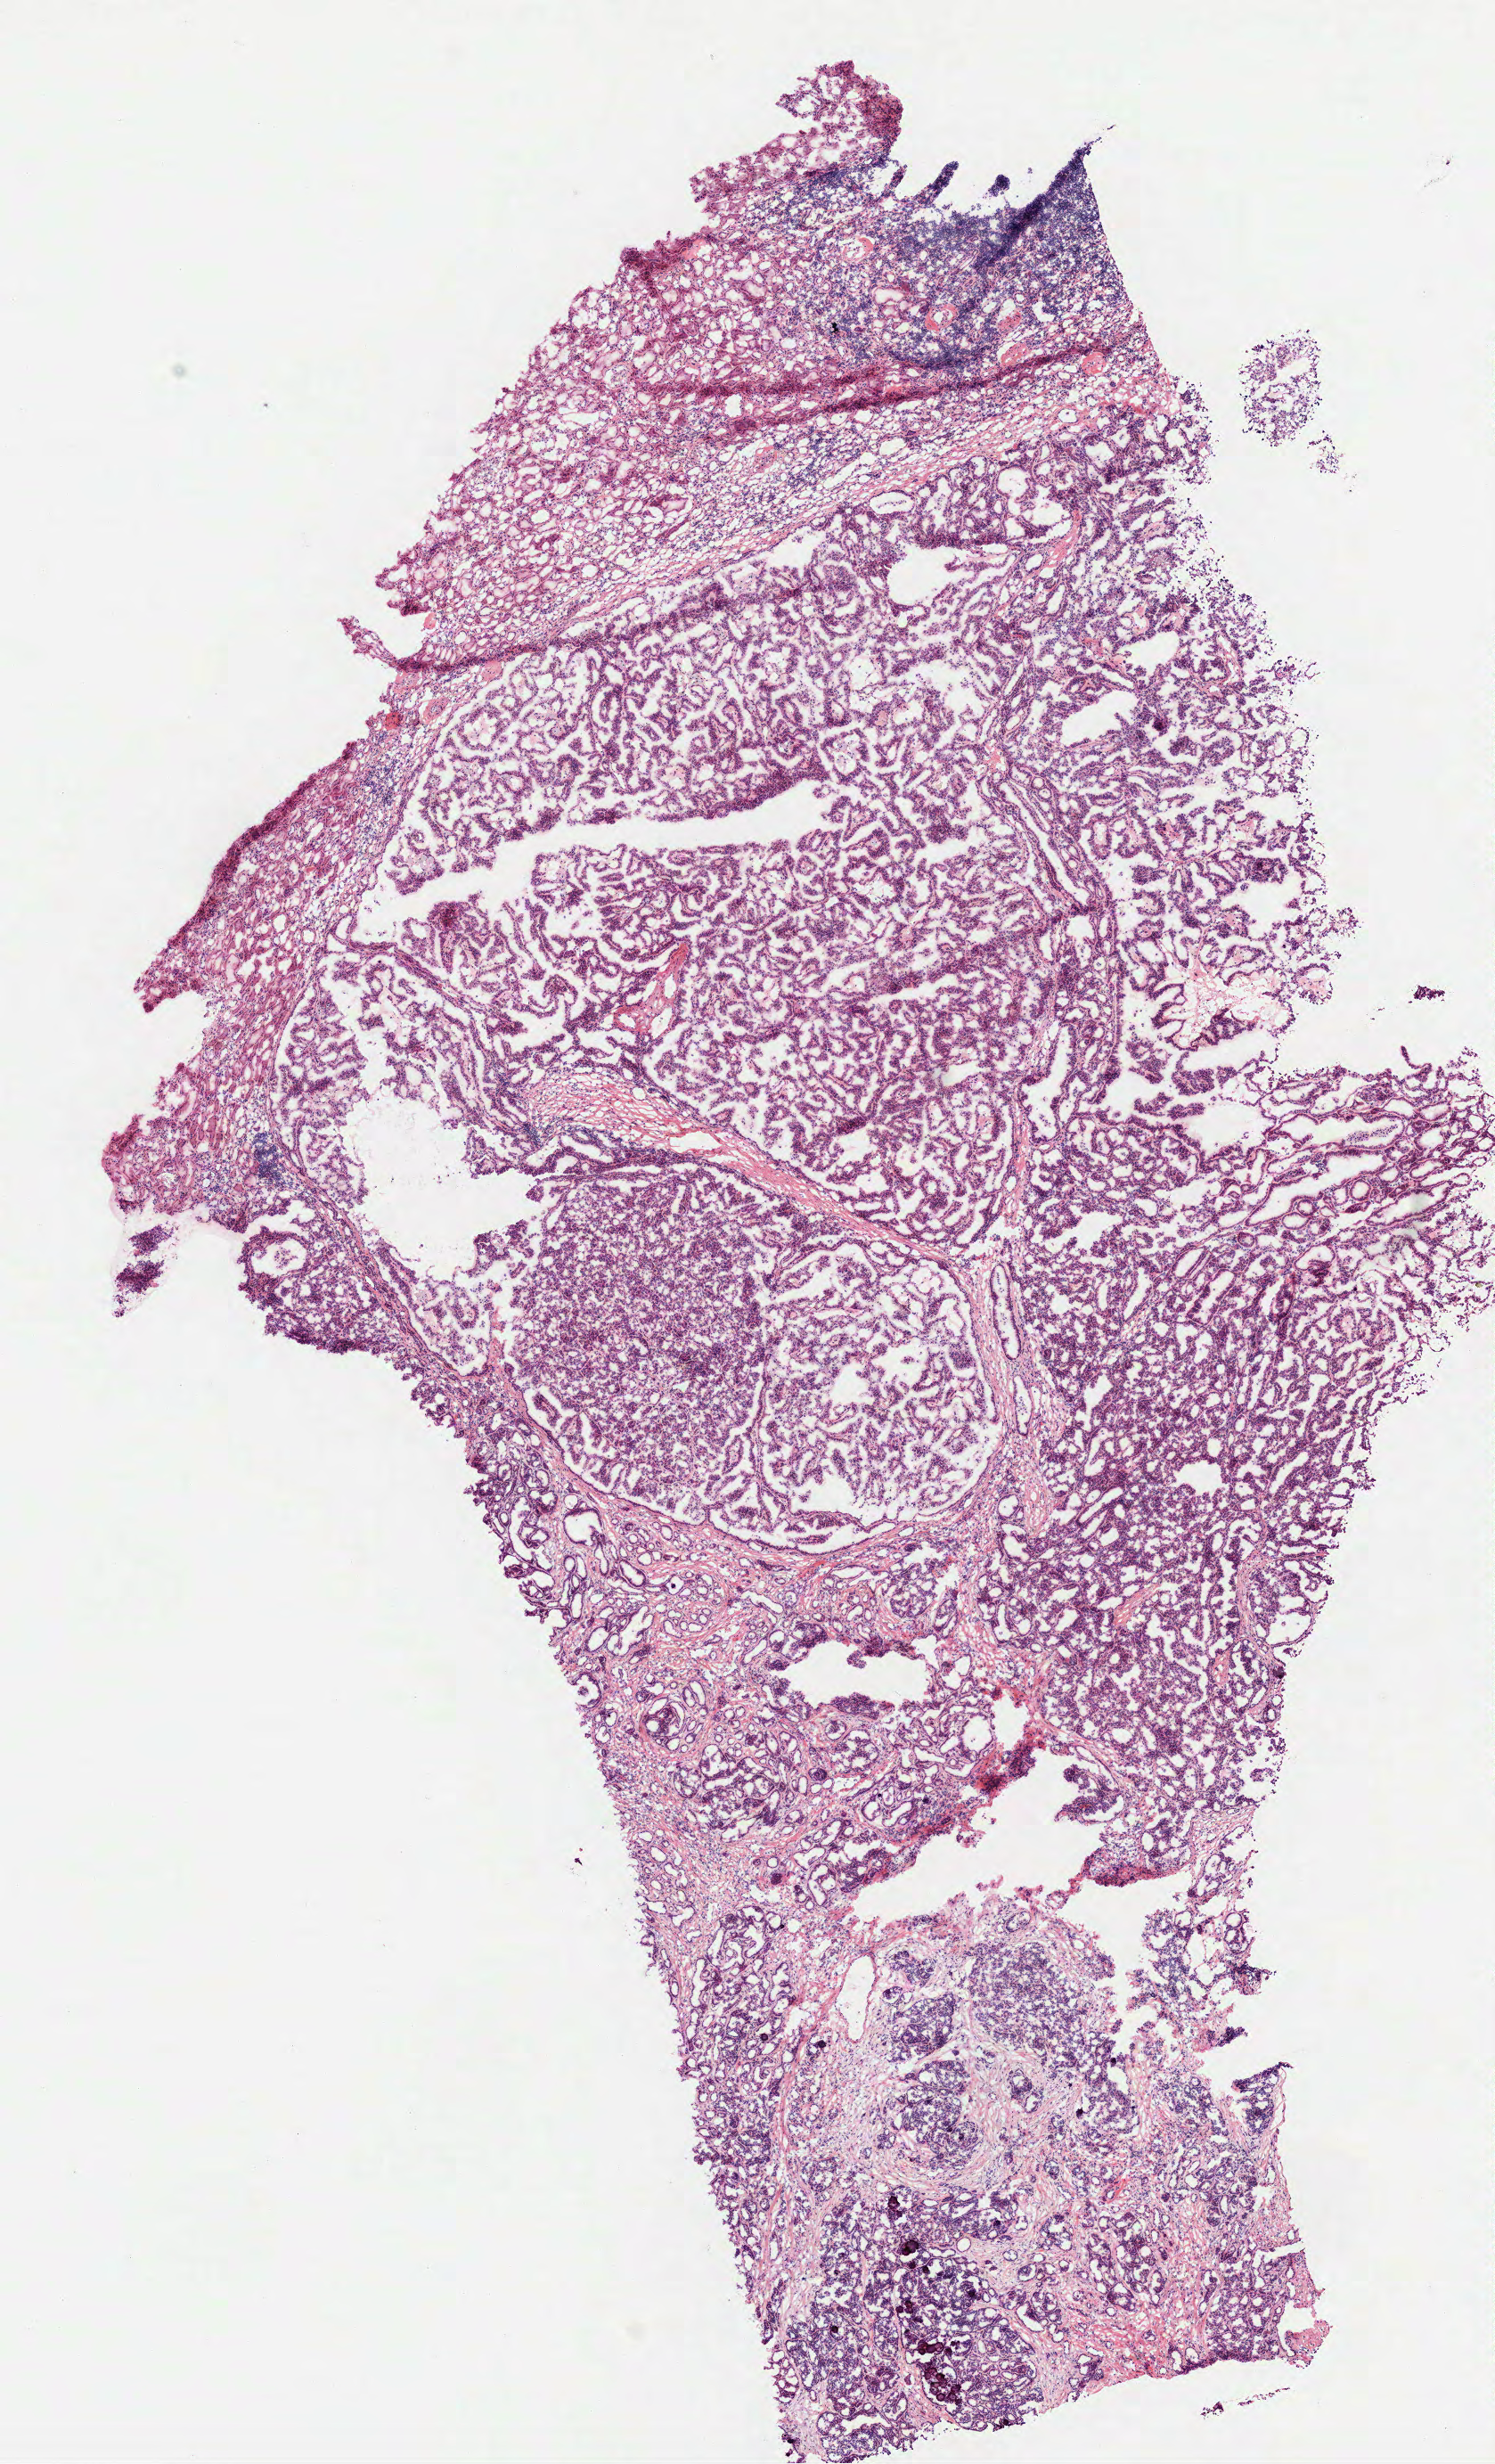
Whole-slide histology image, Hematoxylin and eosin (H&E) stained — low-resolution overview of the scanned area, about 6.8 x 11.2 mm (from a 40x scan); frozen section; kidney, primary tumour sample. Patient: female, age at initial diagnosis 57 years. Pathologist review of this section (percent, as recorded): tumour cells 100%, tumour nuclei 80%, normal cells 0%, stromal cells 0%, necrosis 0%. Inflammatory infiltration, as recorded: lymphocyte infiltration 2%, monocyte infiltration 5%, neutrophil infiltration 0%.
AJCC pathologic stage: III (6th edition). Laterality: right. Diagnosis: Papillary adenocarcinoma, NOS.